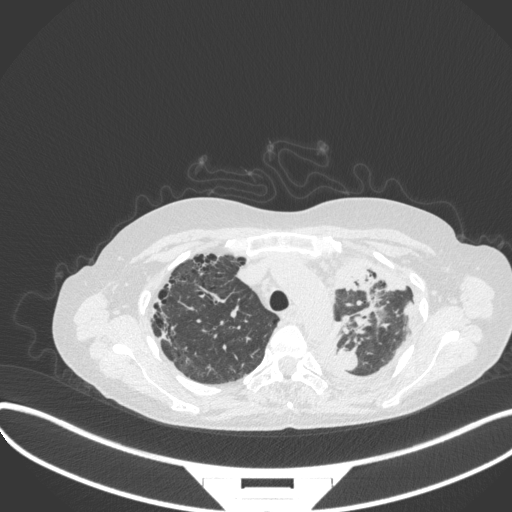
Chest CT, one axial slice. Position 263 of 373 along the scan axis. Reconstruction kernel B31f. 120 kVp. Lung window (W 1500 / L -600 HU). 1 mm slice thickness. 512 × 512 image matrix, field of view 400 × 400 mm. Patient: female, 56 years. Case-level facts recorded for this patient, not image findings: clinical TNM (as recorded): T1 N0 M0.
Annotated regions visible in this slice (rectangle marked by the reading radiologist):
- lung tumour (recorded histology: adenocarcinoma): box from (x=334, y=257) to (x=405, y=325) px